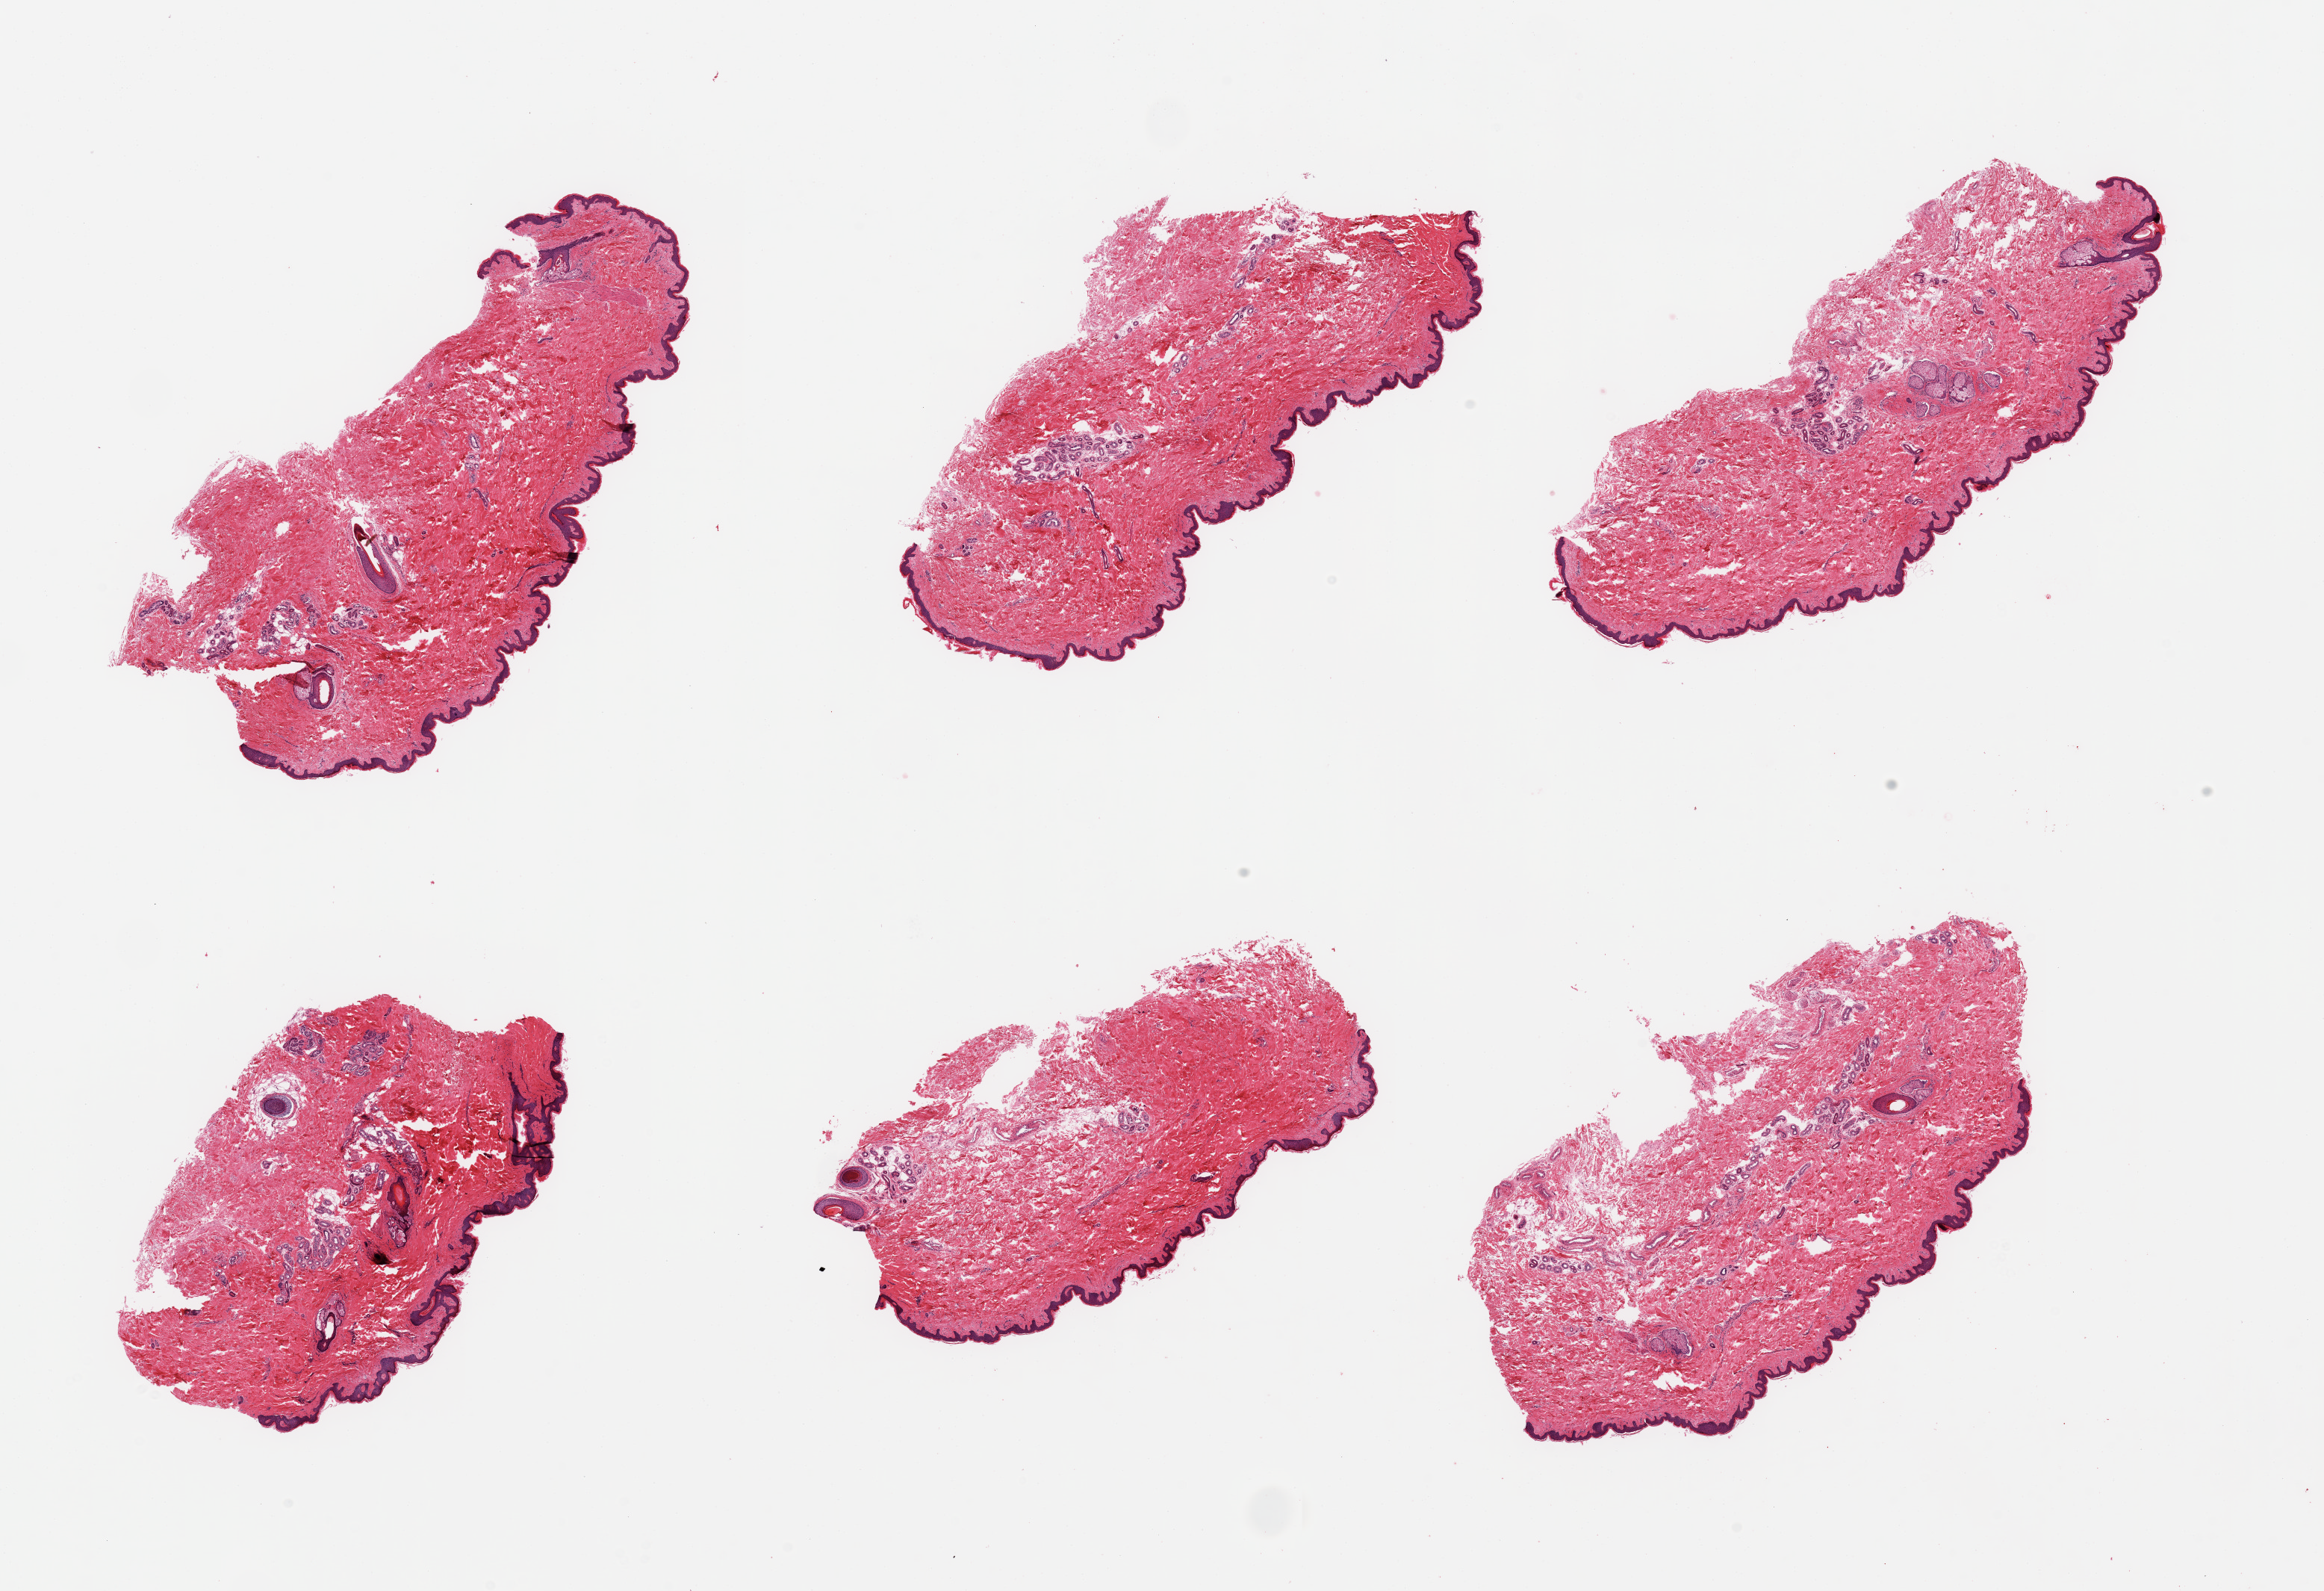
Digitized H&E-stained section, brightfield — shown as a low-resolution overview of the whole scanned area (about 24.6 x 16.8 mm). PAXgene-fixed, paraffin-embedded tissue. Target tissue: skin of suprapubic region. Donor tissue sample. Donor sex: male.
Review note (as recorded): 6 pieces; well trimmed.